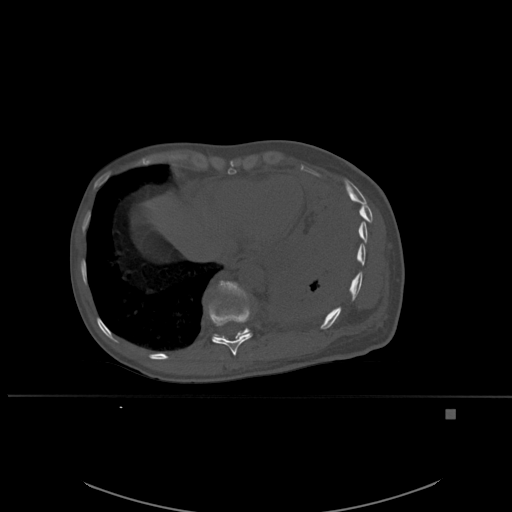
CT including the spine, one axial slice; position 313 of 537 along the scan axis; bone window (W 1800 / L 400 HU); 512 × 512 image matrix, field of view 440 × 440 mm. Female patient, age 45 years. From the clinical record (not read from this slice): primary cancer: lung.
Structures marked on this image (semi-automatically segmented with operator editing):
- T10 vertebra: bounding box [x1, y1, x2, y2] px = [208, 293, 253, 356]
- T11 vertebra: [213, 281, 252, 340]